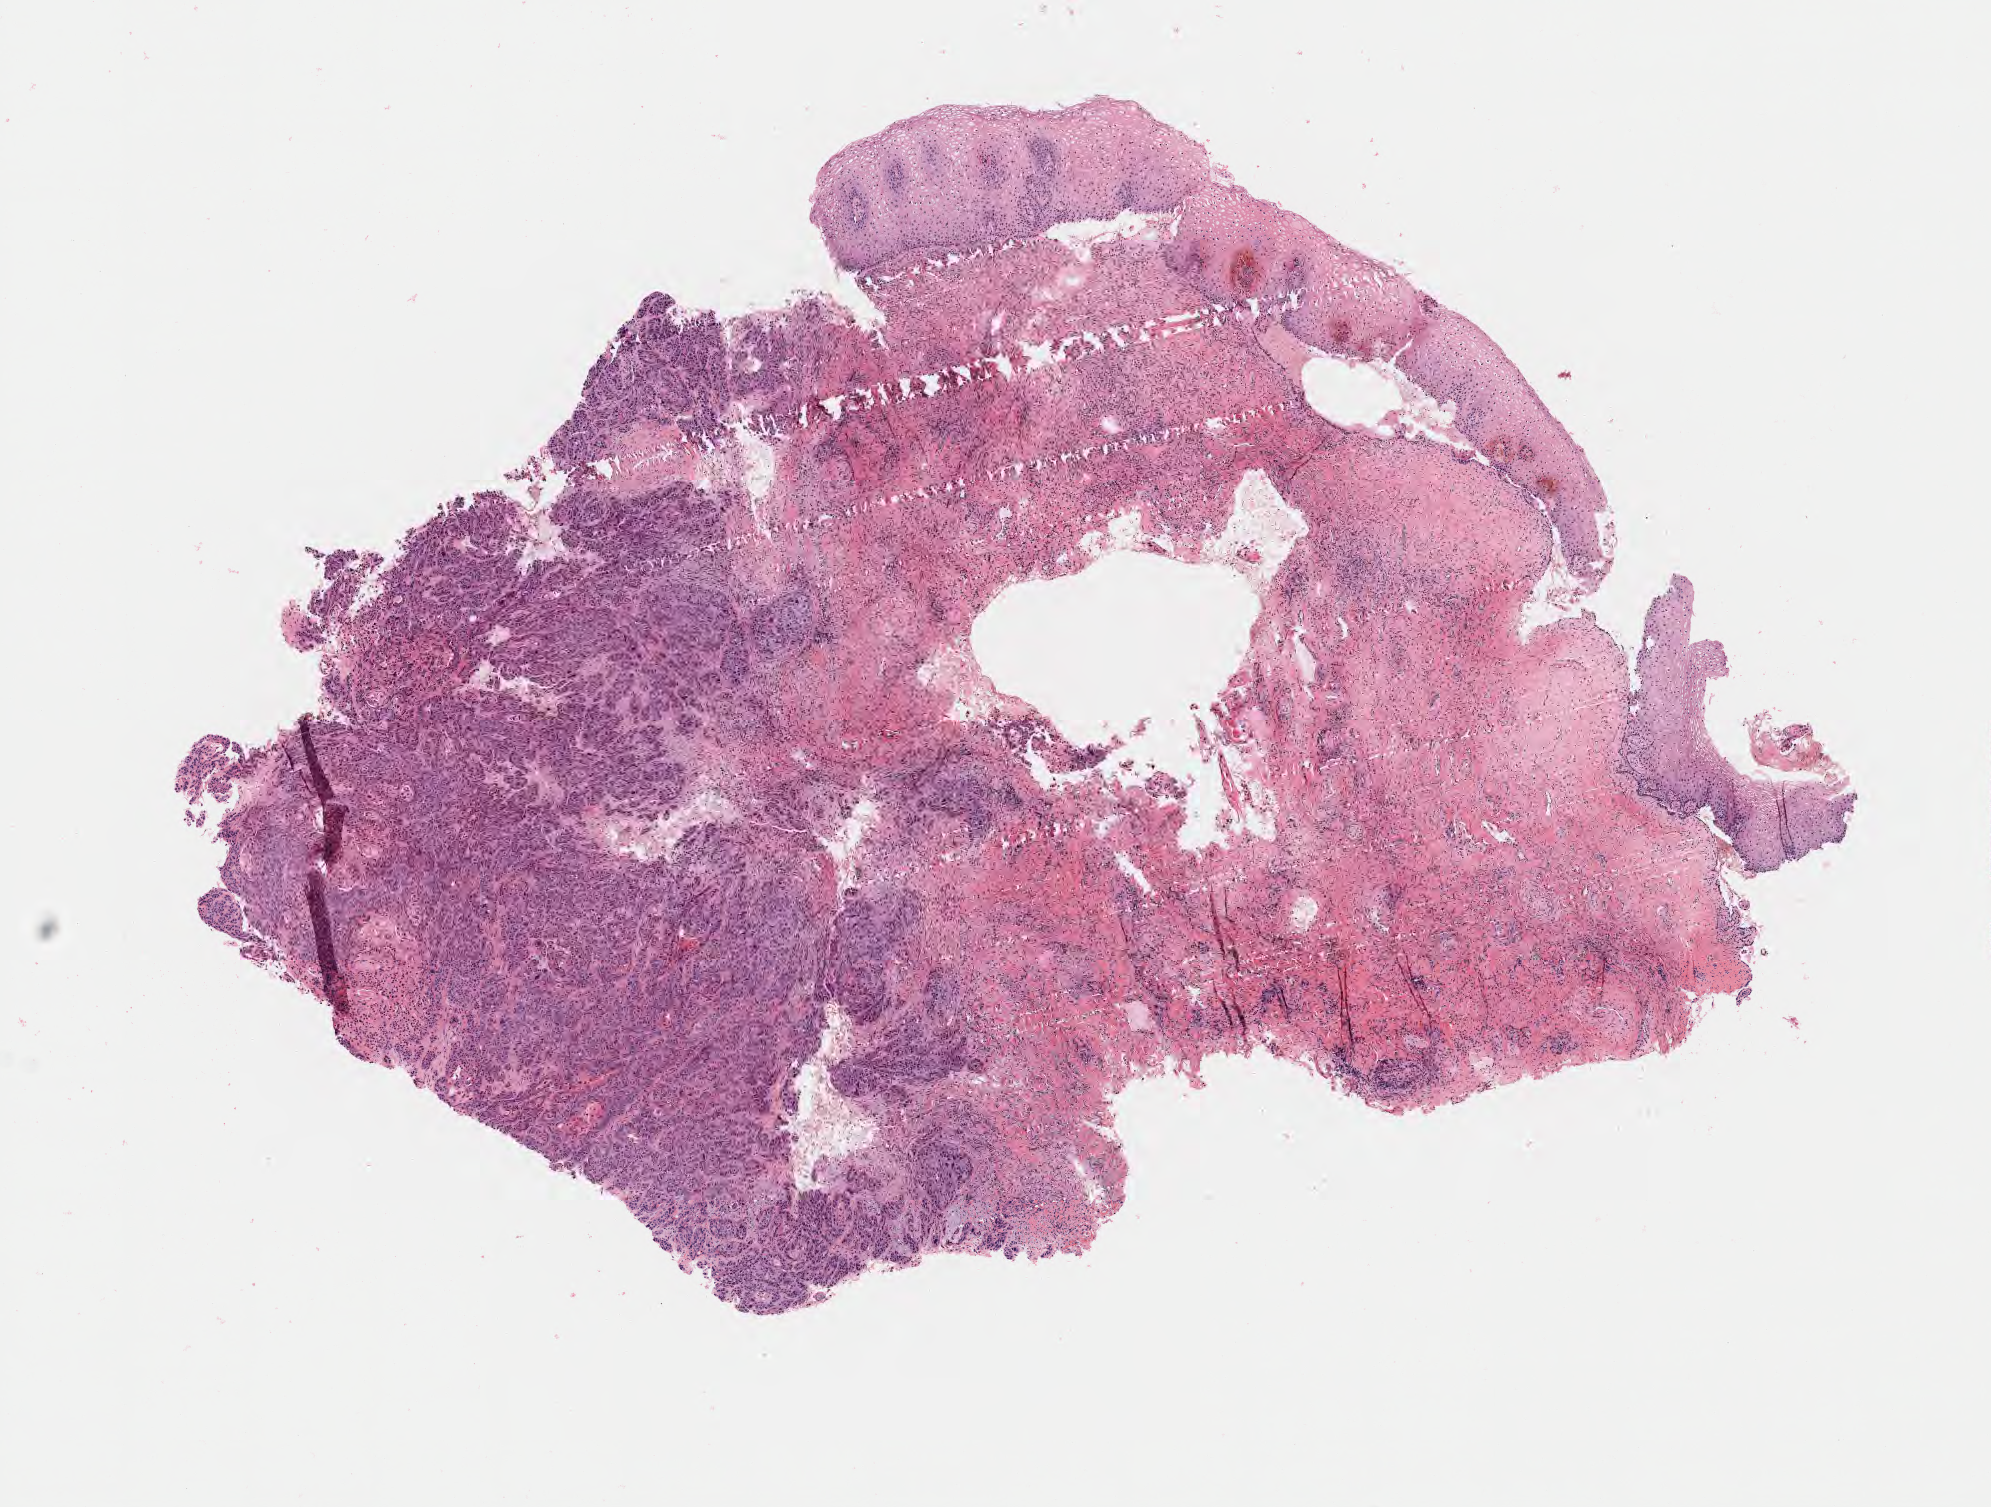
Haematoxylin and eosin whole-slide image, a low-resolution overview of the entire scanned area, about 8.1 x 6.1 mm, specimen: tumor tissue, anatomic site: cervix. Patient: female, 38 years old.
* diagnosis: Squamous cell carcinoma, keratinizing, NOS